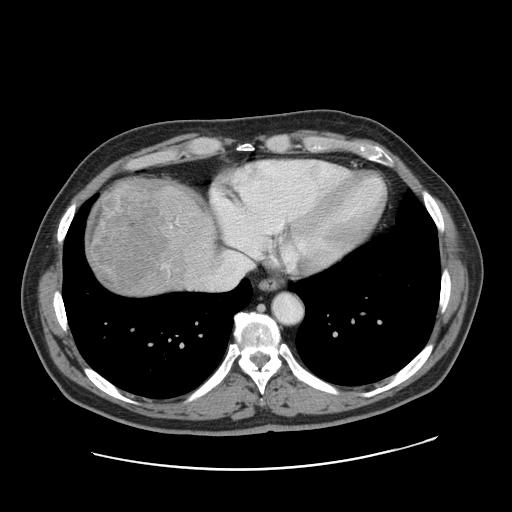
Contrast-enhanced abdominal CT, one axial slice; position 150 of 178 along the scan axis; 120 kVp; intravenous contrast given; soft-tissue window (W 400 / L 40 HU); 512 × 512 image matrix, field of view 403 × 403 mm. Male patient, age 63 years. From the clinical record (not read from this slice): diagnosis: colorectal cancer liver metastases, imaged before liver resection; multiple liver metastases: yes.
Outlined on this slice (manually delineated by an expert):
- liver: box from (x=84, y=179) to (x=219, y=297) px
- planned liver remnant (the part of the liver to remain after resection): (x=186, y=194)–(x=217, y=246)
- liver metastasis: (x=88, y=183)–(x=165, y=290)